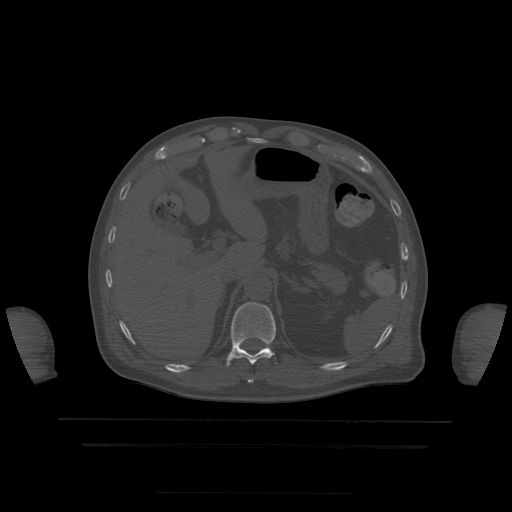
CT including the spine, one axial slice; position 218 of 522 along the scan axis; bone window (W 1800 / L 400 HU); 512 × 512 image matrix, field of view 436 × 436 mm. Patient age 68 years. Case-level facts recorded for this patient, not image findings: primary cancer: urothelial.
Annotated regions visible in this slice (semi-automatically segmented with operator editing):
- T10 vertebra: bounding box <248,379,254,383> (left, top, right, bottom; pixels)
- T11 vertebra: <227,302,276,367>